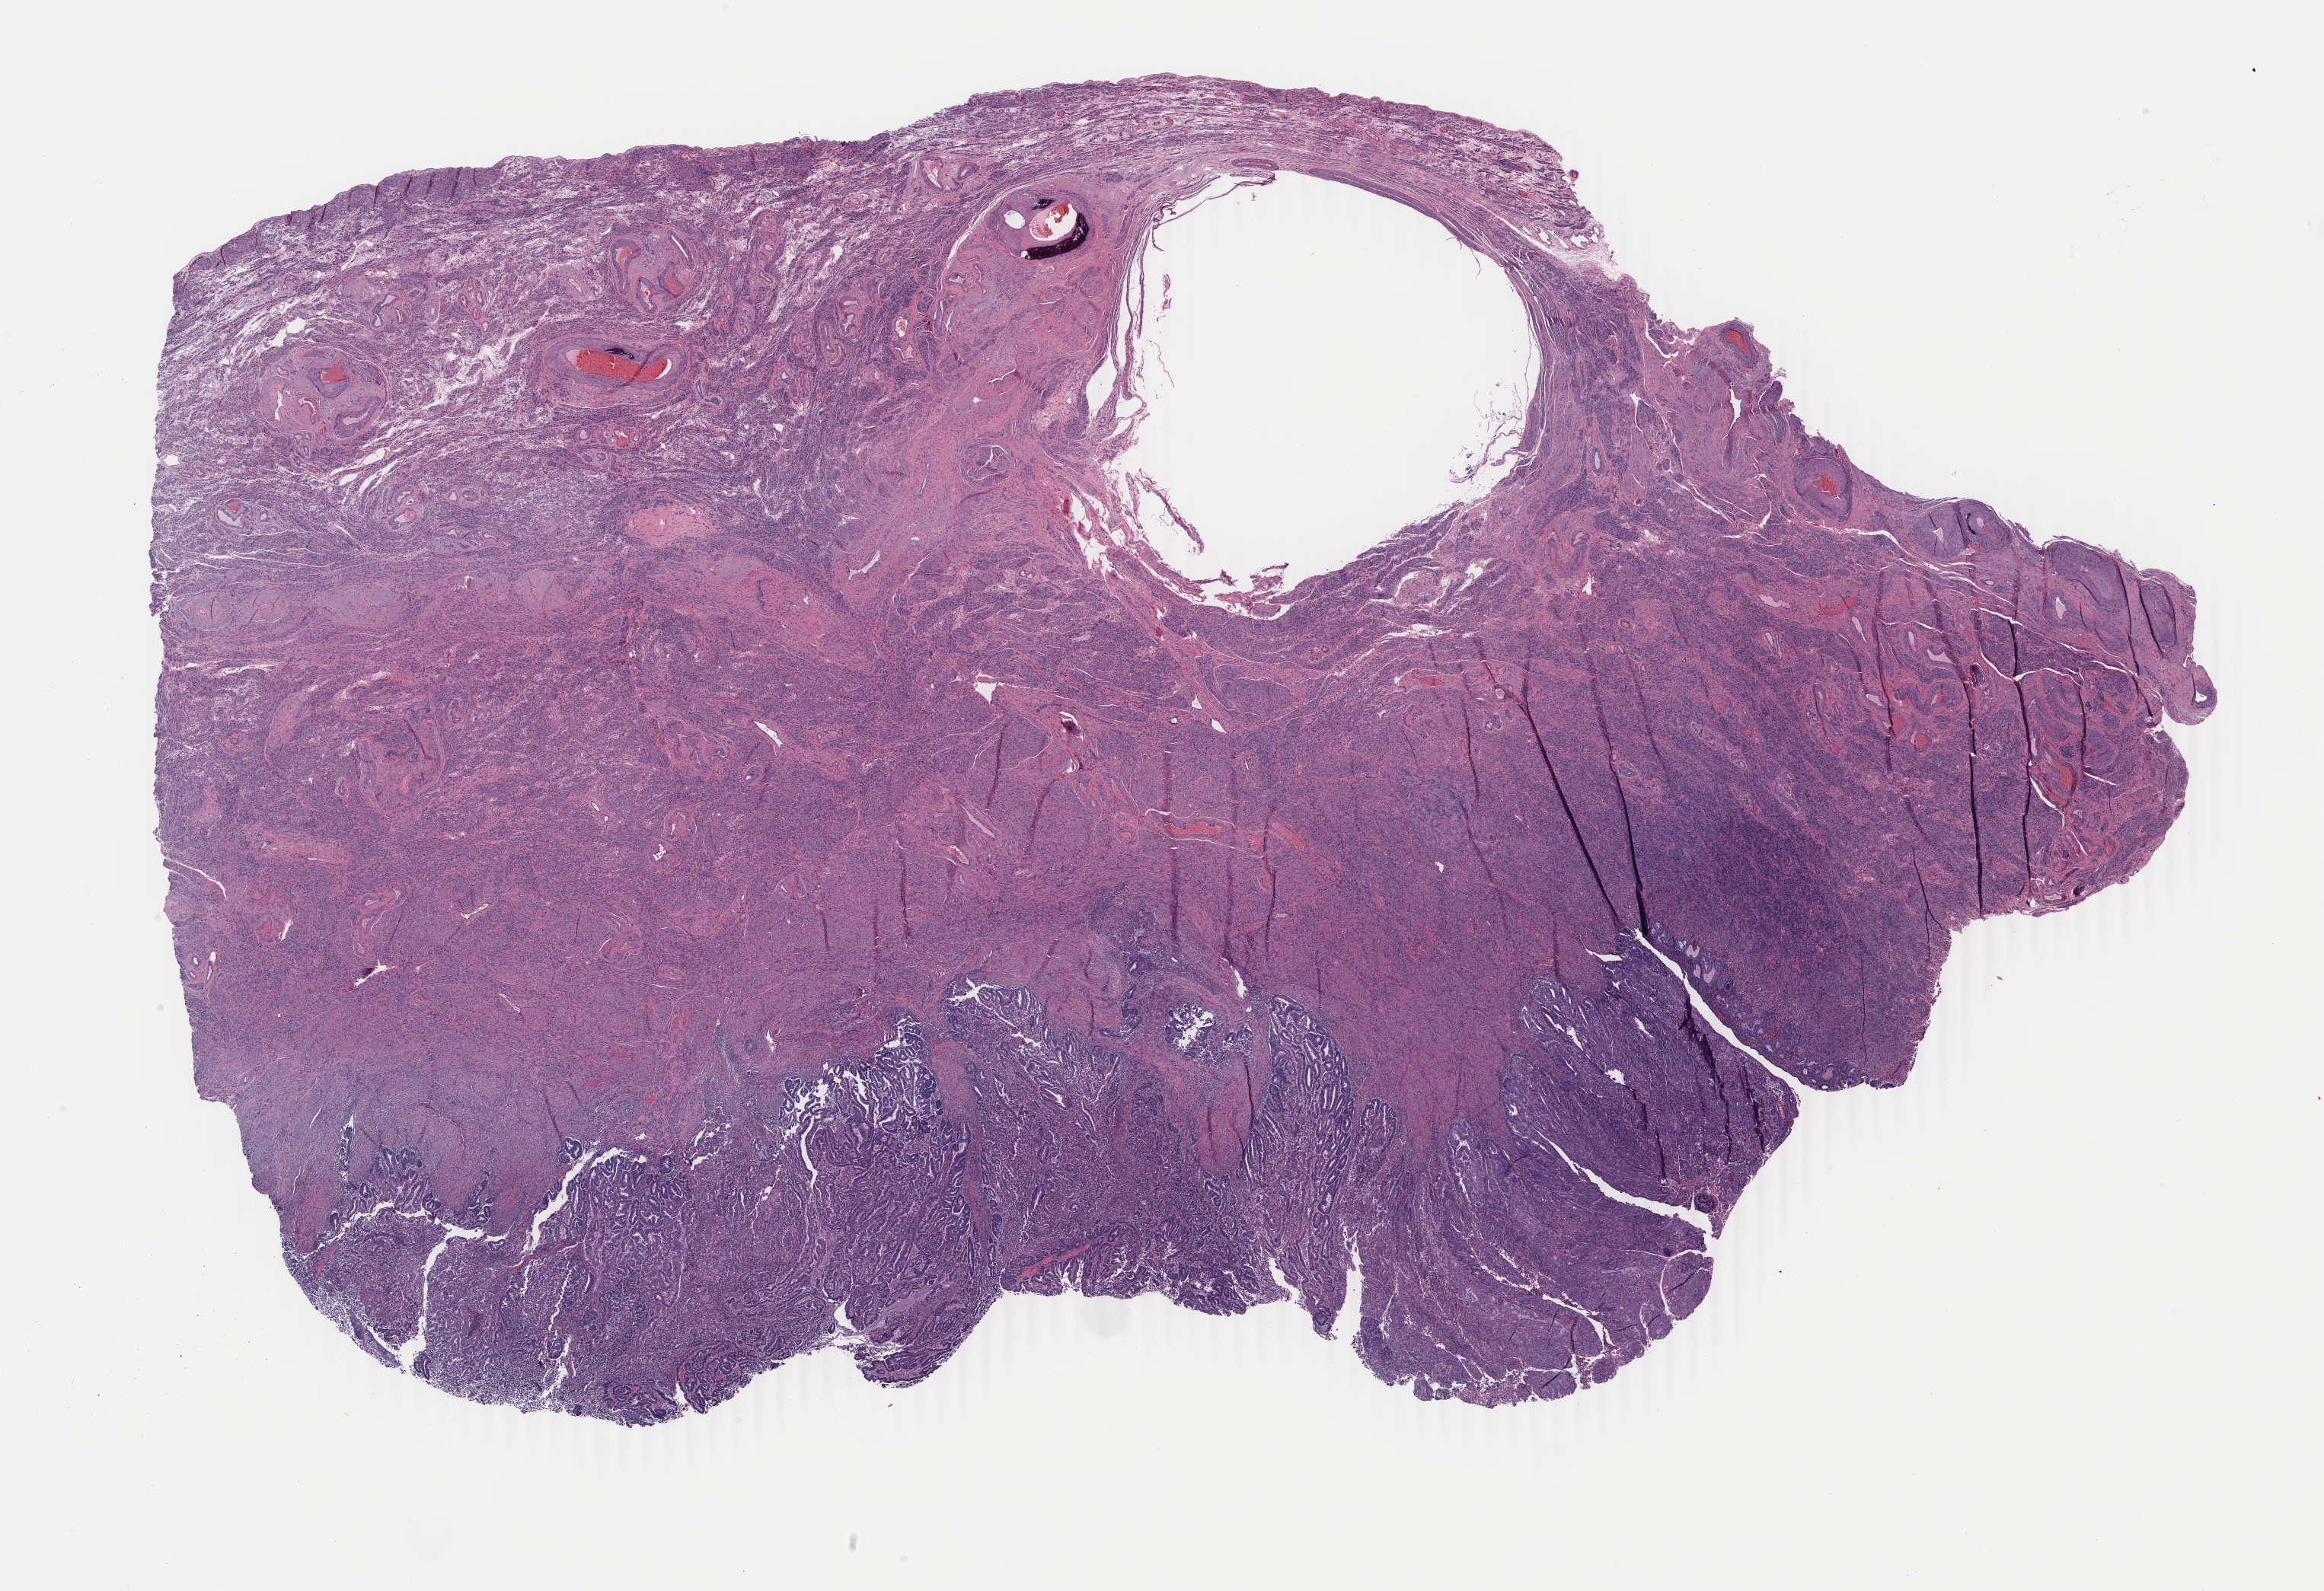
H&E whole-slide image, a low-resolution overview of the entire scanned area, about 24.3 x 16.6 mm (slide scanned at 40x). Formalin-fixed paraffin-embedded (FFPE) diagnostic section. Sample: primary tumour, uterus. Female, age 77 years at initial diagnosis. Histologic grade: G1 (well differentiated).
• diagnosis: Endometrioid adenocarcinoma, NOS (endometrium)
• FIGO stage: IA